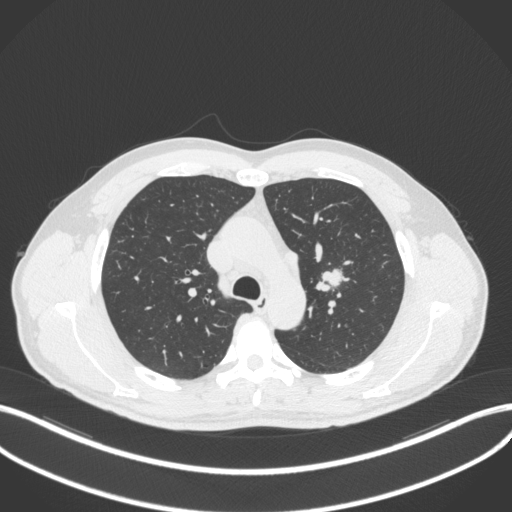
Chest CT, one axial slice. Slice 299 of 383 in the series (ordered by position). 120 kVp. Lung window (W 1500 / L -600 HU). 1 mm slice thickness. 512 × 512 image matrix, field of view 400 × 400 mm. Male patient, age 50 years. Case-level facts recorded for this patient, not image findings: clinical TNM (as recorded): T1c N1 M1b.
Outlined on this slice (bounding box drawn by a radiologist):
- lung tumour (recorded histology: squamous cell carcinoma): bounding box [x1, y1, x2, y2] px = [314, 264, 346, 295]